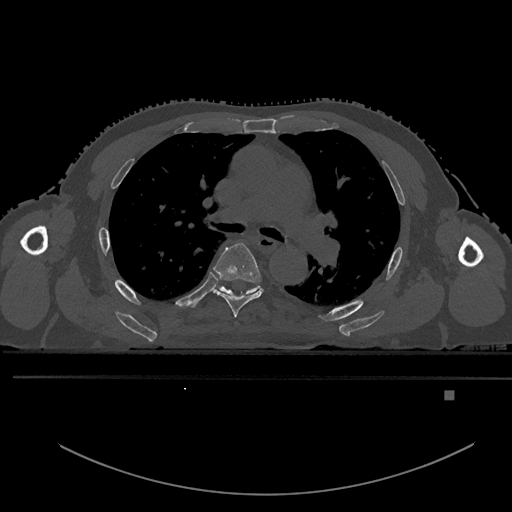
CT including the spine, one axial slice; position 346 of 969 along the scan axis; bone window (W 1800 / L 400 HU); 0.5 mm slice thickness; 512 × 512 image matrix, field of view 456 × 456 mm. Patient: male, 82 years. From the clinical record (not read from this slice): primary cancer: prostate; vertebrae with lytic lesions (as recorded): T11, T9, T8, T2.
Outlined on this slice (semi-automatic segmentation, software-assisted and operator-edited):
- T5 vertebra: bounding box [x1, y1, x2, y2] px = [213, 242, 263, 318]
- T6 vertebra: [216, 285, 261, 297]